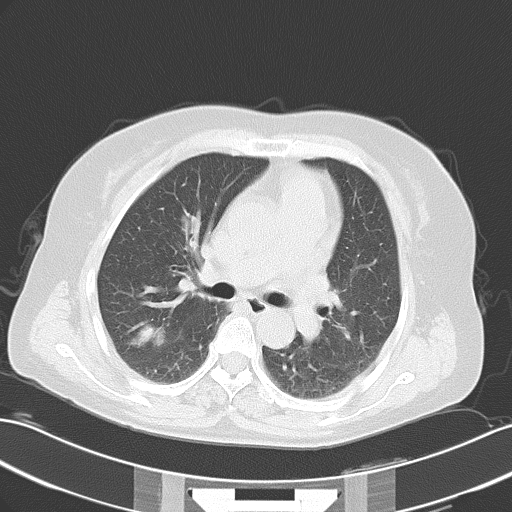
Chest CT, one axial slice. Position 30 of 49 along the scan axis. 120 kVp. Lung window (W 1500 / L -600 HU). 5 mm slice thickness. 512 × 512 image matrix, field of view 353 × 353 mm. Female patient, age 52 years. From the clinical record (not read from this slice): clinical TNM (as recorded): T1c N3 M1a.
Annotated regions visible in this slice (bounding box drawn by a radiologist):
- lung tumour (recorded histology: adenocarcinoma): bounding box (x1, y1, x2, y2) in pixels: (125, 325, 174, 351)